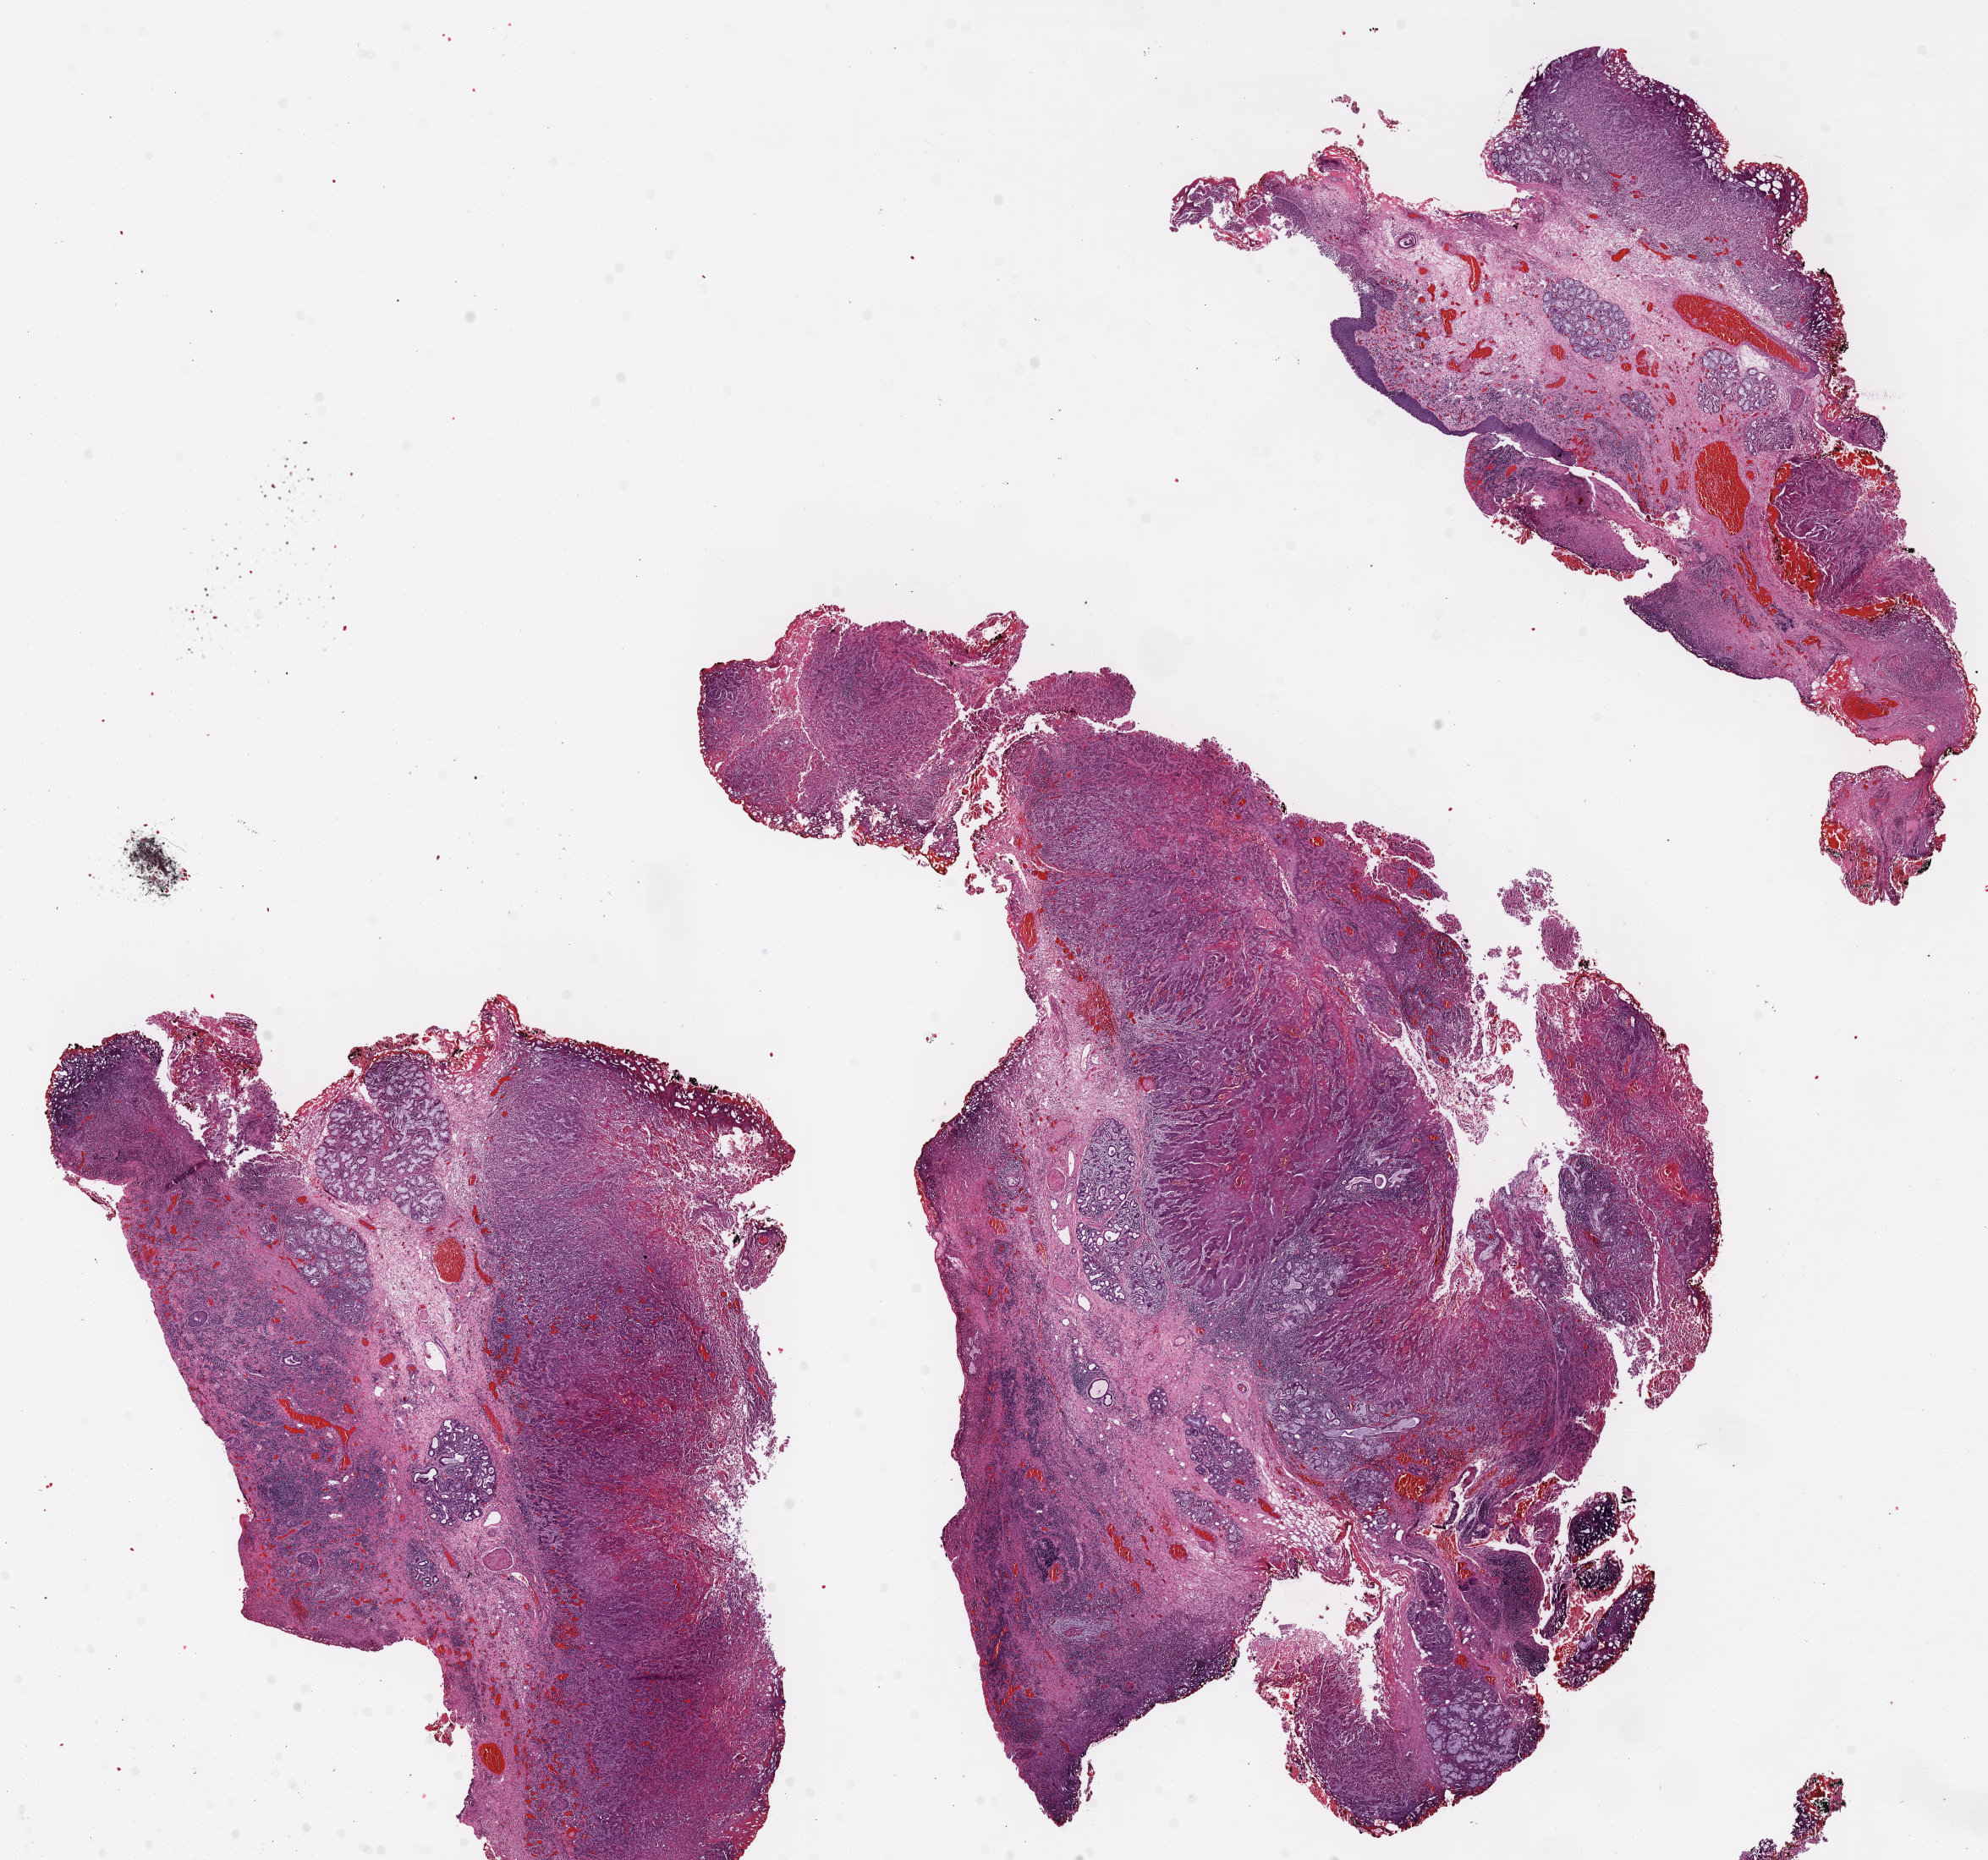
Digitized H&E tissue section (whole slide) — low-resolution overview of the scanned area, about 18.5 x 17.3 mm; formalin-fixed paraffin-embedded (FFPE) diagnostic section; sample: primary tumour, head and neck. Male patient; age at initial diagnosis 60 years. Histologic grade: G3 (poorly differentiated).
Laterality: left. AJCC pathologic stage: IVA. Diagnosis: Squamous cell carcinoma, NOS (larynx, NOS).